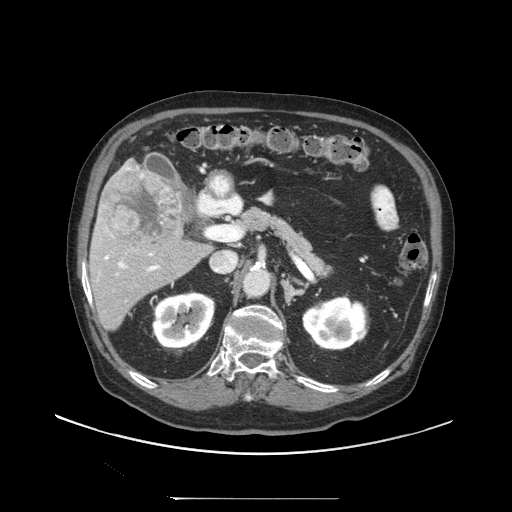
Contrast-enhanced abdominal CT (liver protocol), one axial slice. Position 53 of 97 along the scan axis. 140 kVp. Soft-tissue window (W 400 / L 40 HU). 2.5 mm slice thickness. 512 × 512 image matrix, field of view 450 × 450 mm. From the clinical record (not read from this slice): diagnosis: hepatocellular carcinoma (patient treated with transarterial chemoembolisation; whether this scan precedes or follows treatment is not stated here); TNM stage (as recorded): Stage-IIIC.
Structures marked on this image (semi-automatically segmented with operator editing):
- liver parenchyma outside the tumour (the mass and vessels are separate outlines, so this box may not span the whole liver): box from (x=90, y=159) to (x=209, y=330) px
- mass: (x=102, y=169)–(x=183, y=253)
- liver vessels: (x=98, y=167)–(x=160, y=275)